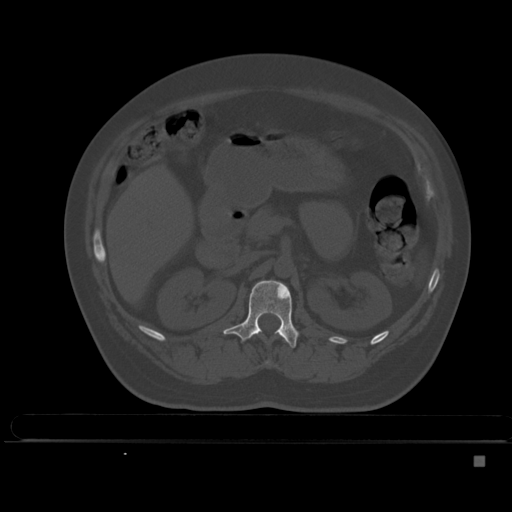
CT including the spine, one axial slice; bone window (W 1800 / L 400 HU); 1.5 mm slice thickness; 512 × 512 image matrix, field of view 404 × 404 mm. Female patient, age 33 years. Case-level facts recorded for this patient, not image findings: primary cancer: breast.
Structures marked on this image (semi-automatically segmented with operator editing):
- L1 vertebra: box from (x=223, y=280) to (x=299, y=349) px
- T12 vertebra: (x=266, y=339)–(x=287, y=364)